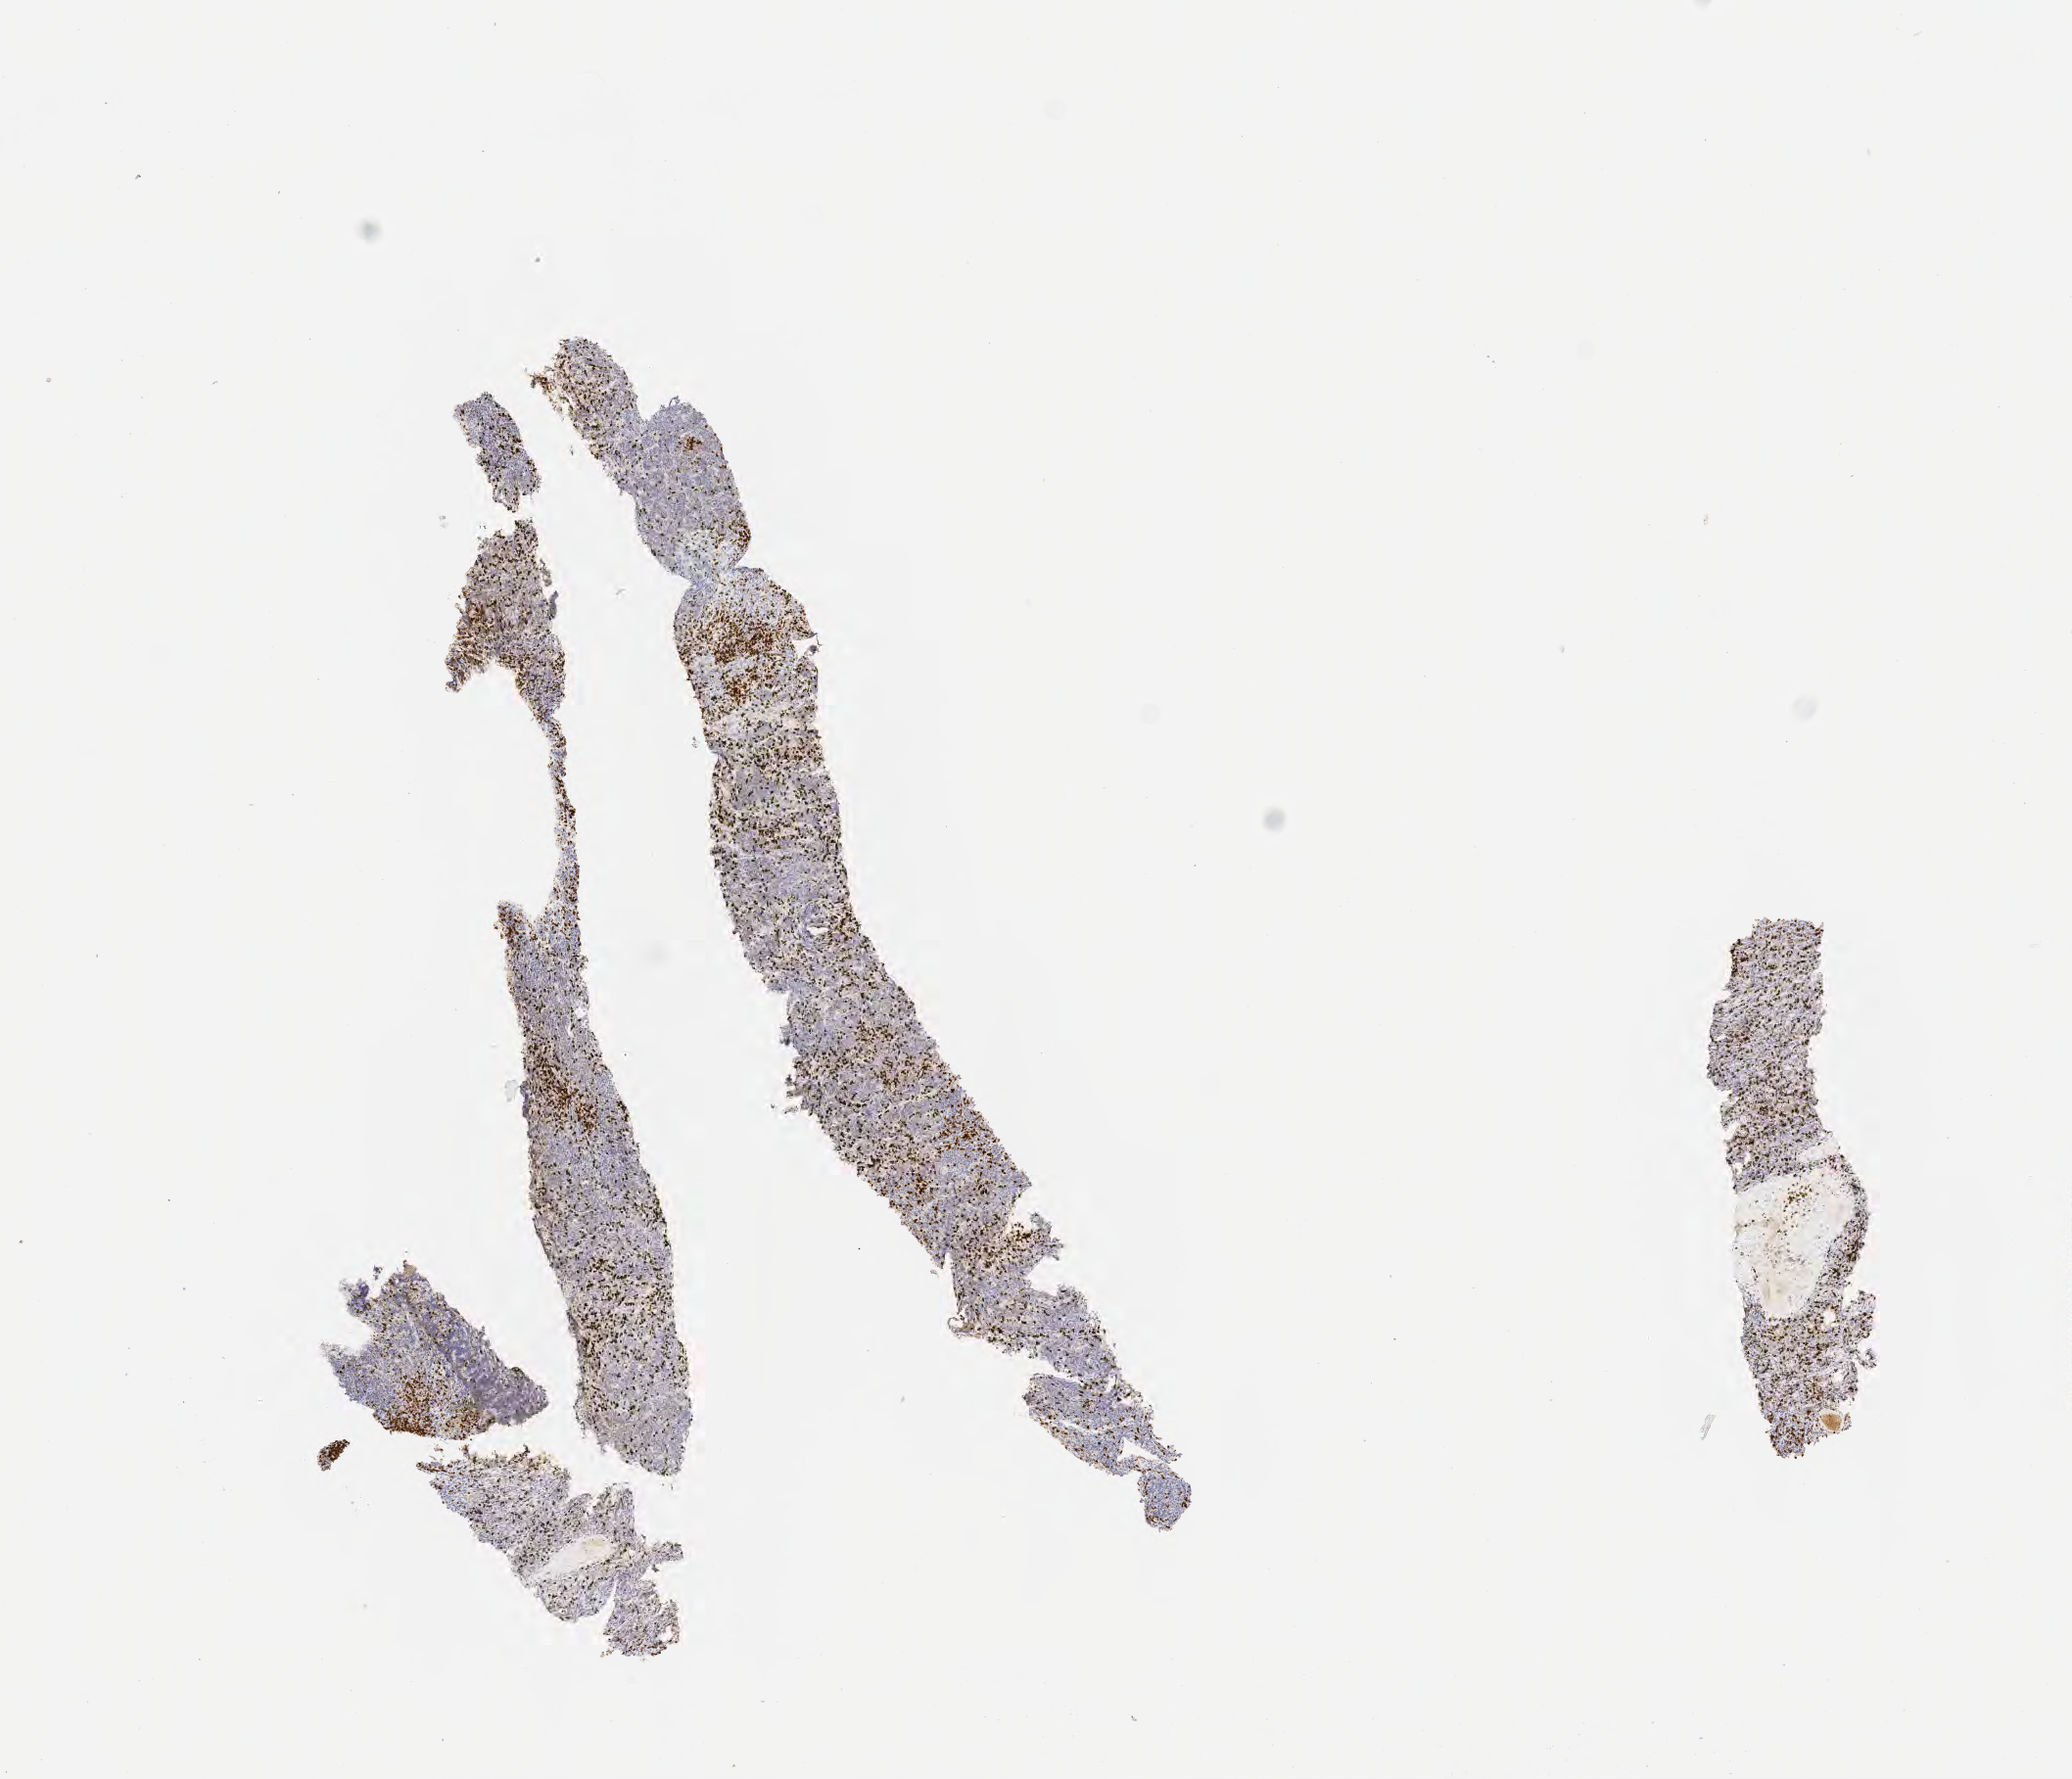
Whole-slide image, immunohistochemical stain for CD3 — whole scanned area (about 8.6 x 7.3 mm) shown as a low-resolution overview, tumor tissue. Male patient, age 13 years.
Diagnosis: Diffuse large B-cell lymphoma, NOS.